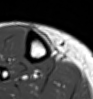
MRI of an extremity soft-tissue mass, one axial slice. MR volume resampled by the dataset authors to the PET/CT grid (not the native acquisition matrix). 3.27 mm slice thickness. 93 × 99 image matrix, field of view 91 × 97 mm. Female patient. Case-level facts recorded for this patient, not image findings: histological type: undifferentiated – high grade; grade: high; site of the primary tumour: right thigh.
Outlined on this slice (expert contour drawn on MRI and transferred to this co-registered scan by the dataset authors):
- gross tumour volume (mass): box from (x=43, y=39) to (x=46, y=42) px